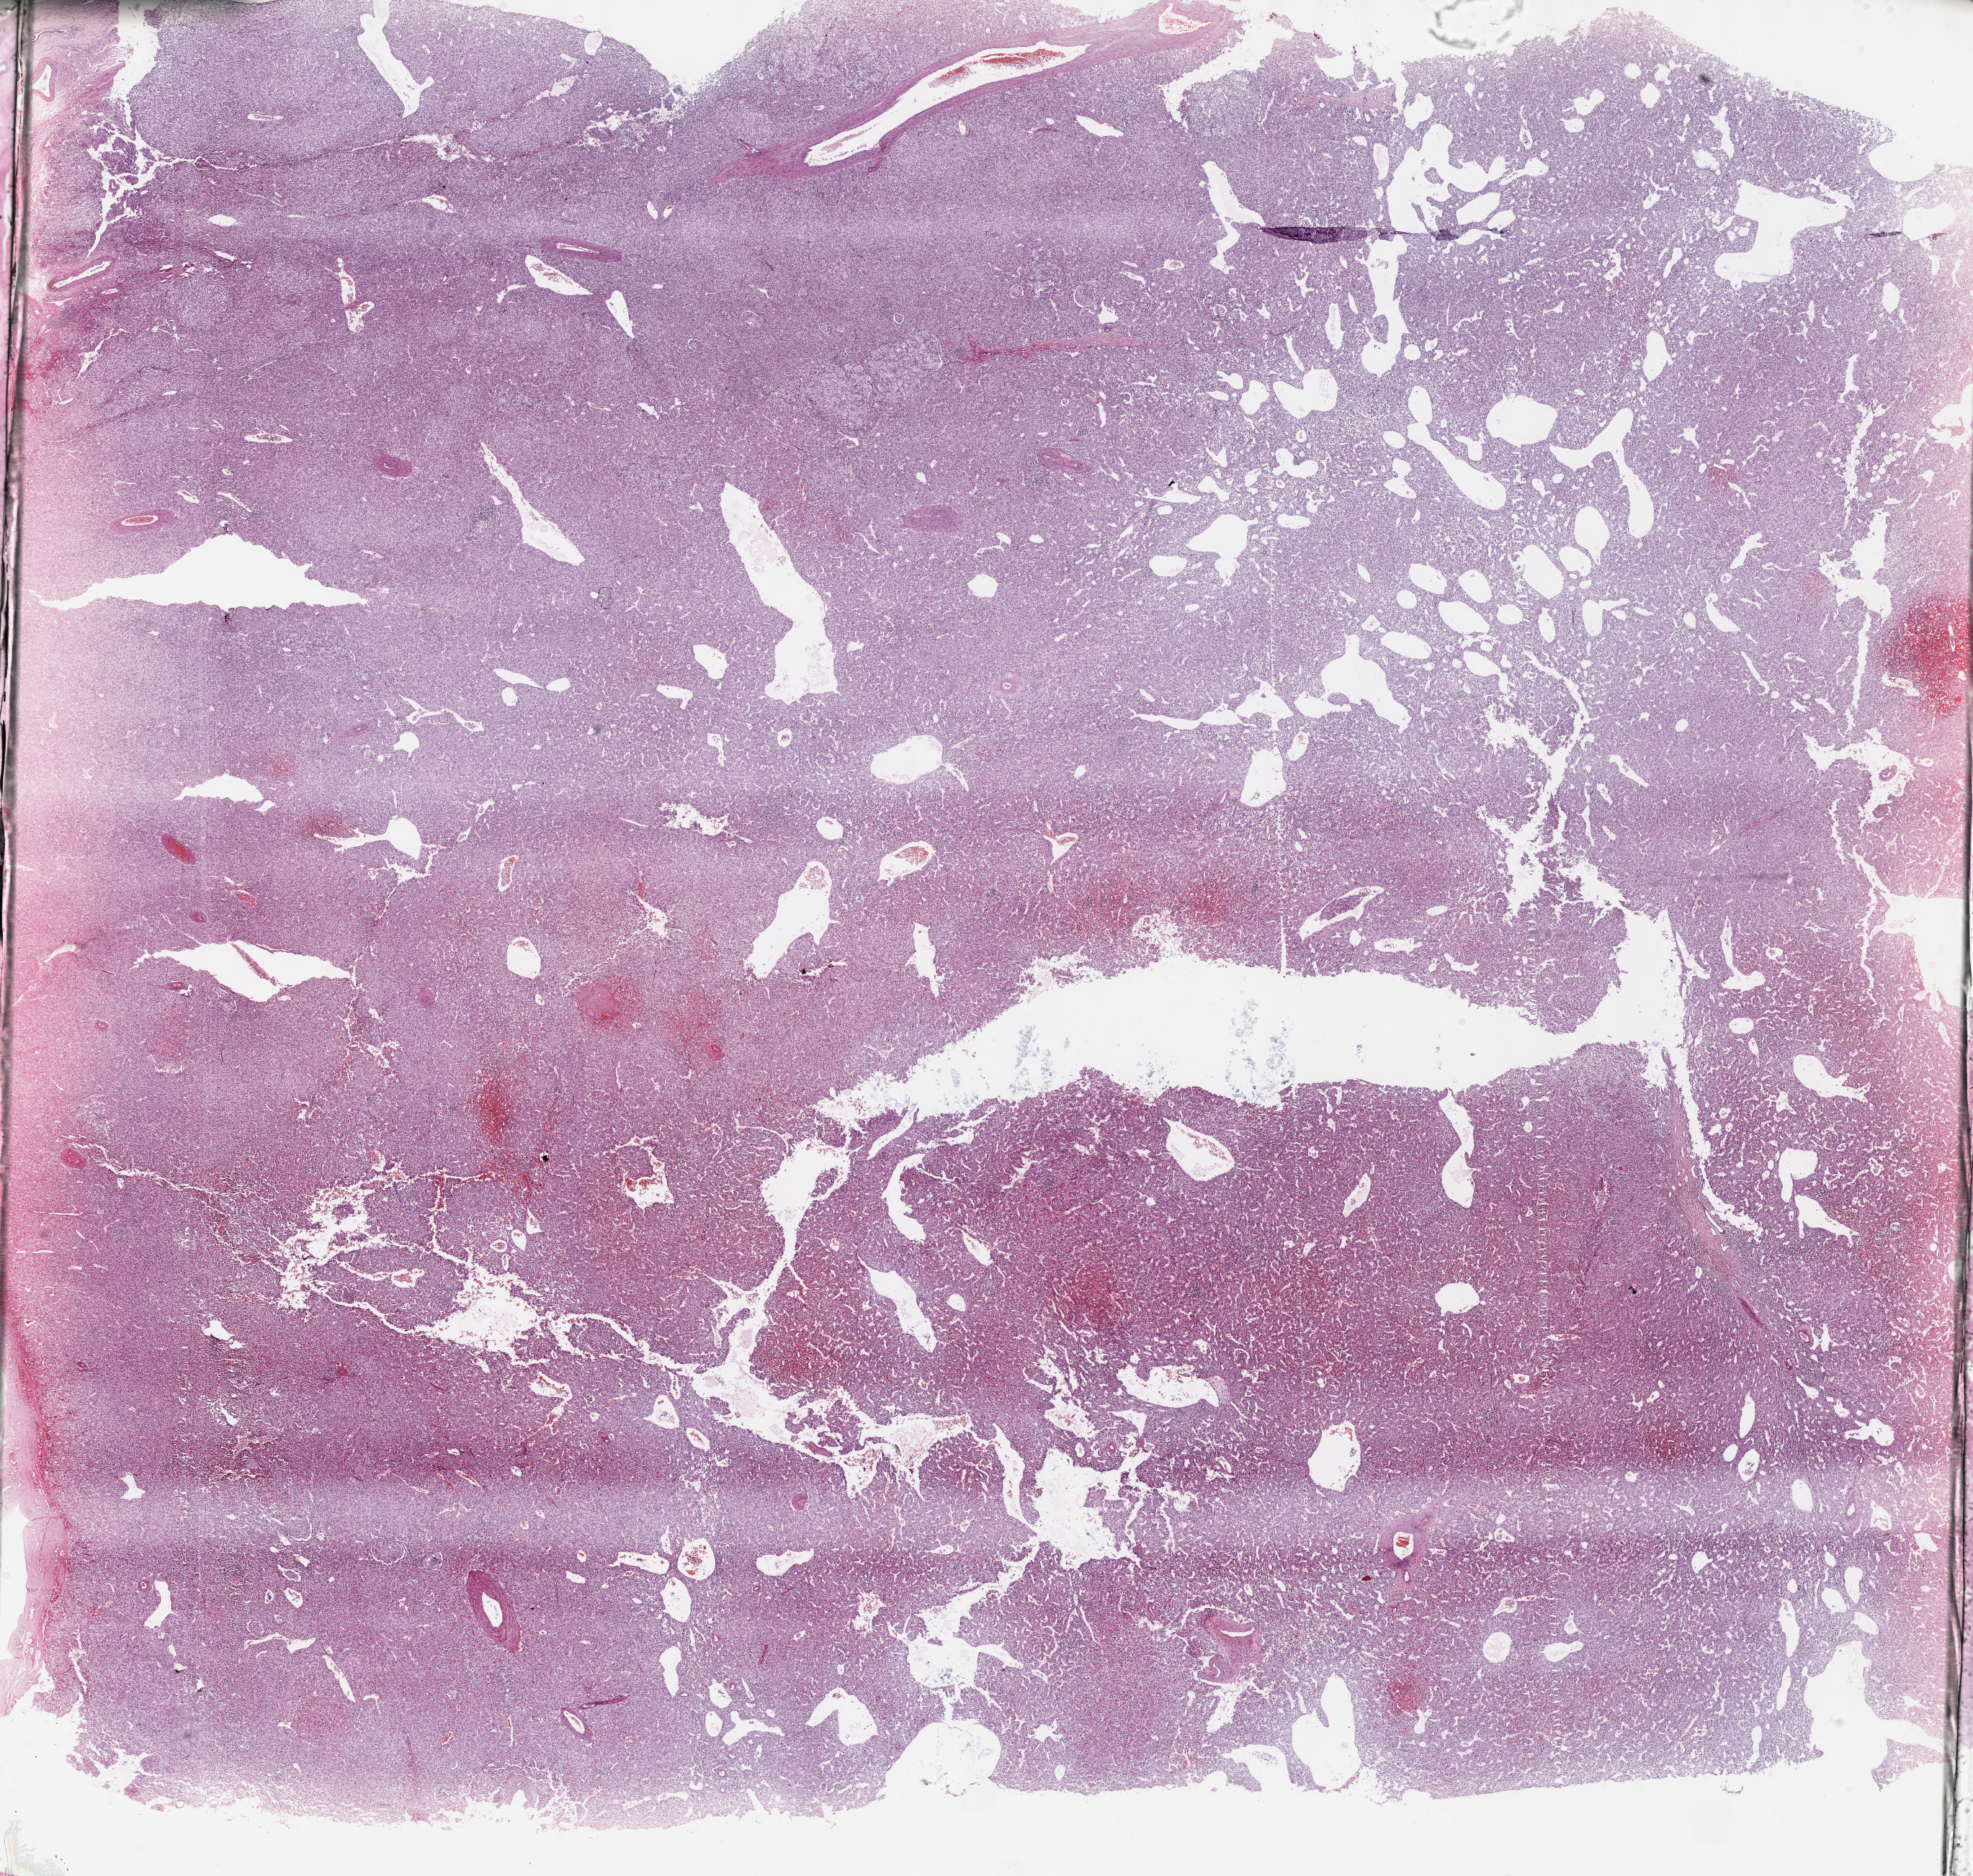
Digitized Hematoxylin and eosin (H&E) stained tissue section (whole slide), low-resolution overview of the scanned area, about 22.1 x 21.0 mm; formalin-fixed paraffin-embedded (FFPE) diagnostic section; liver, primary tumour sample. Patient: male, age at initial diagnosis 57 years. Histologic grade: G2 (moderately differentiated).
Diagnosis: Hepatocellular carcinoma, NOS. TNM: T3 N0 M0. AJCC pathologic stage: IIIA (6th edition).